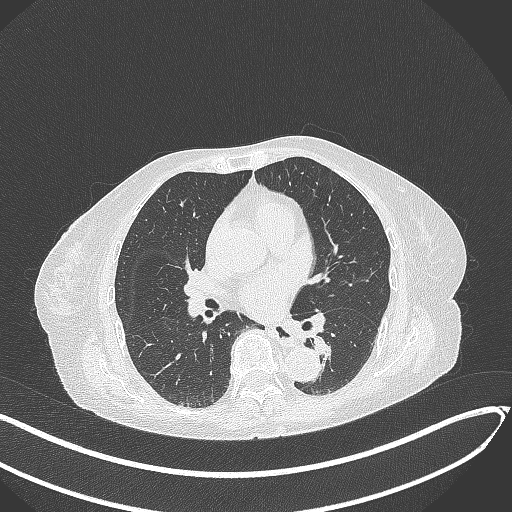
Chest CT, one axial slice. Position 129 of 324 along the scan axis. Lung window (W 1500 / L -600 HU). 1 mm slice thickness. 512 × 512 image matrix, field of view 400 × 400 mm. Patient: female, 82 years. Case-level facts recorded for this patient, not image findings: clinical TNM (as recorded): T1b N0 M1.
Annotated regions visible in this slice (bounding box drawn by a radiologist):
- lung tumour (recorded histology: adenocarcinoma): bounding box <310,332,343,372> (left, top, right, bottom; pixels)